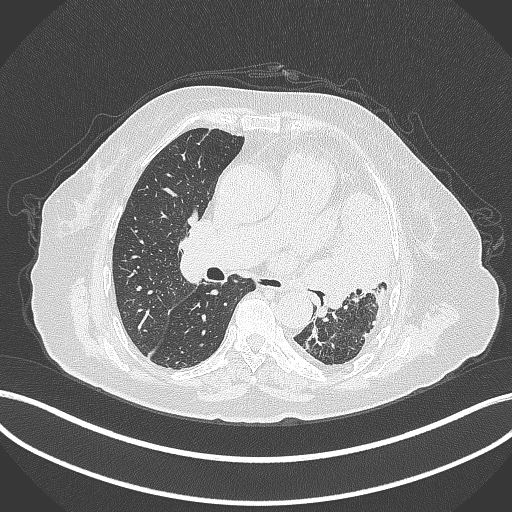
Chest CT, one axial slice; 120 kVp; lung window (W 1500 / L -600 HU); 1 mm slice thickness; 512 × 512 image matrix, field of view 400 × 400 mm. Female patient, age 75 years. From the clinical record (not read from this slice): clinical TNM (as recorded): T3 N3 M1.
Structures marked on this image (rectangle marked by the reading radiologist):
- lung tumour (recorded histology: adenocarcinoma): bounding box [x1, y1, x2, y2] px = [294, 193, 394, 303]